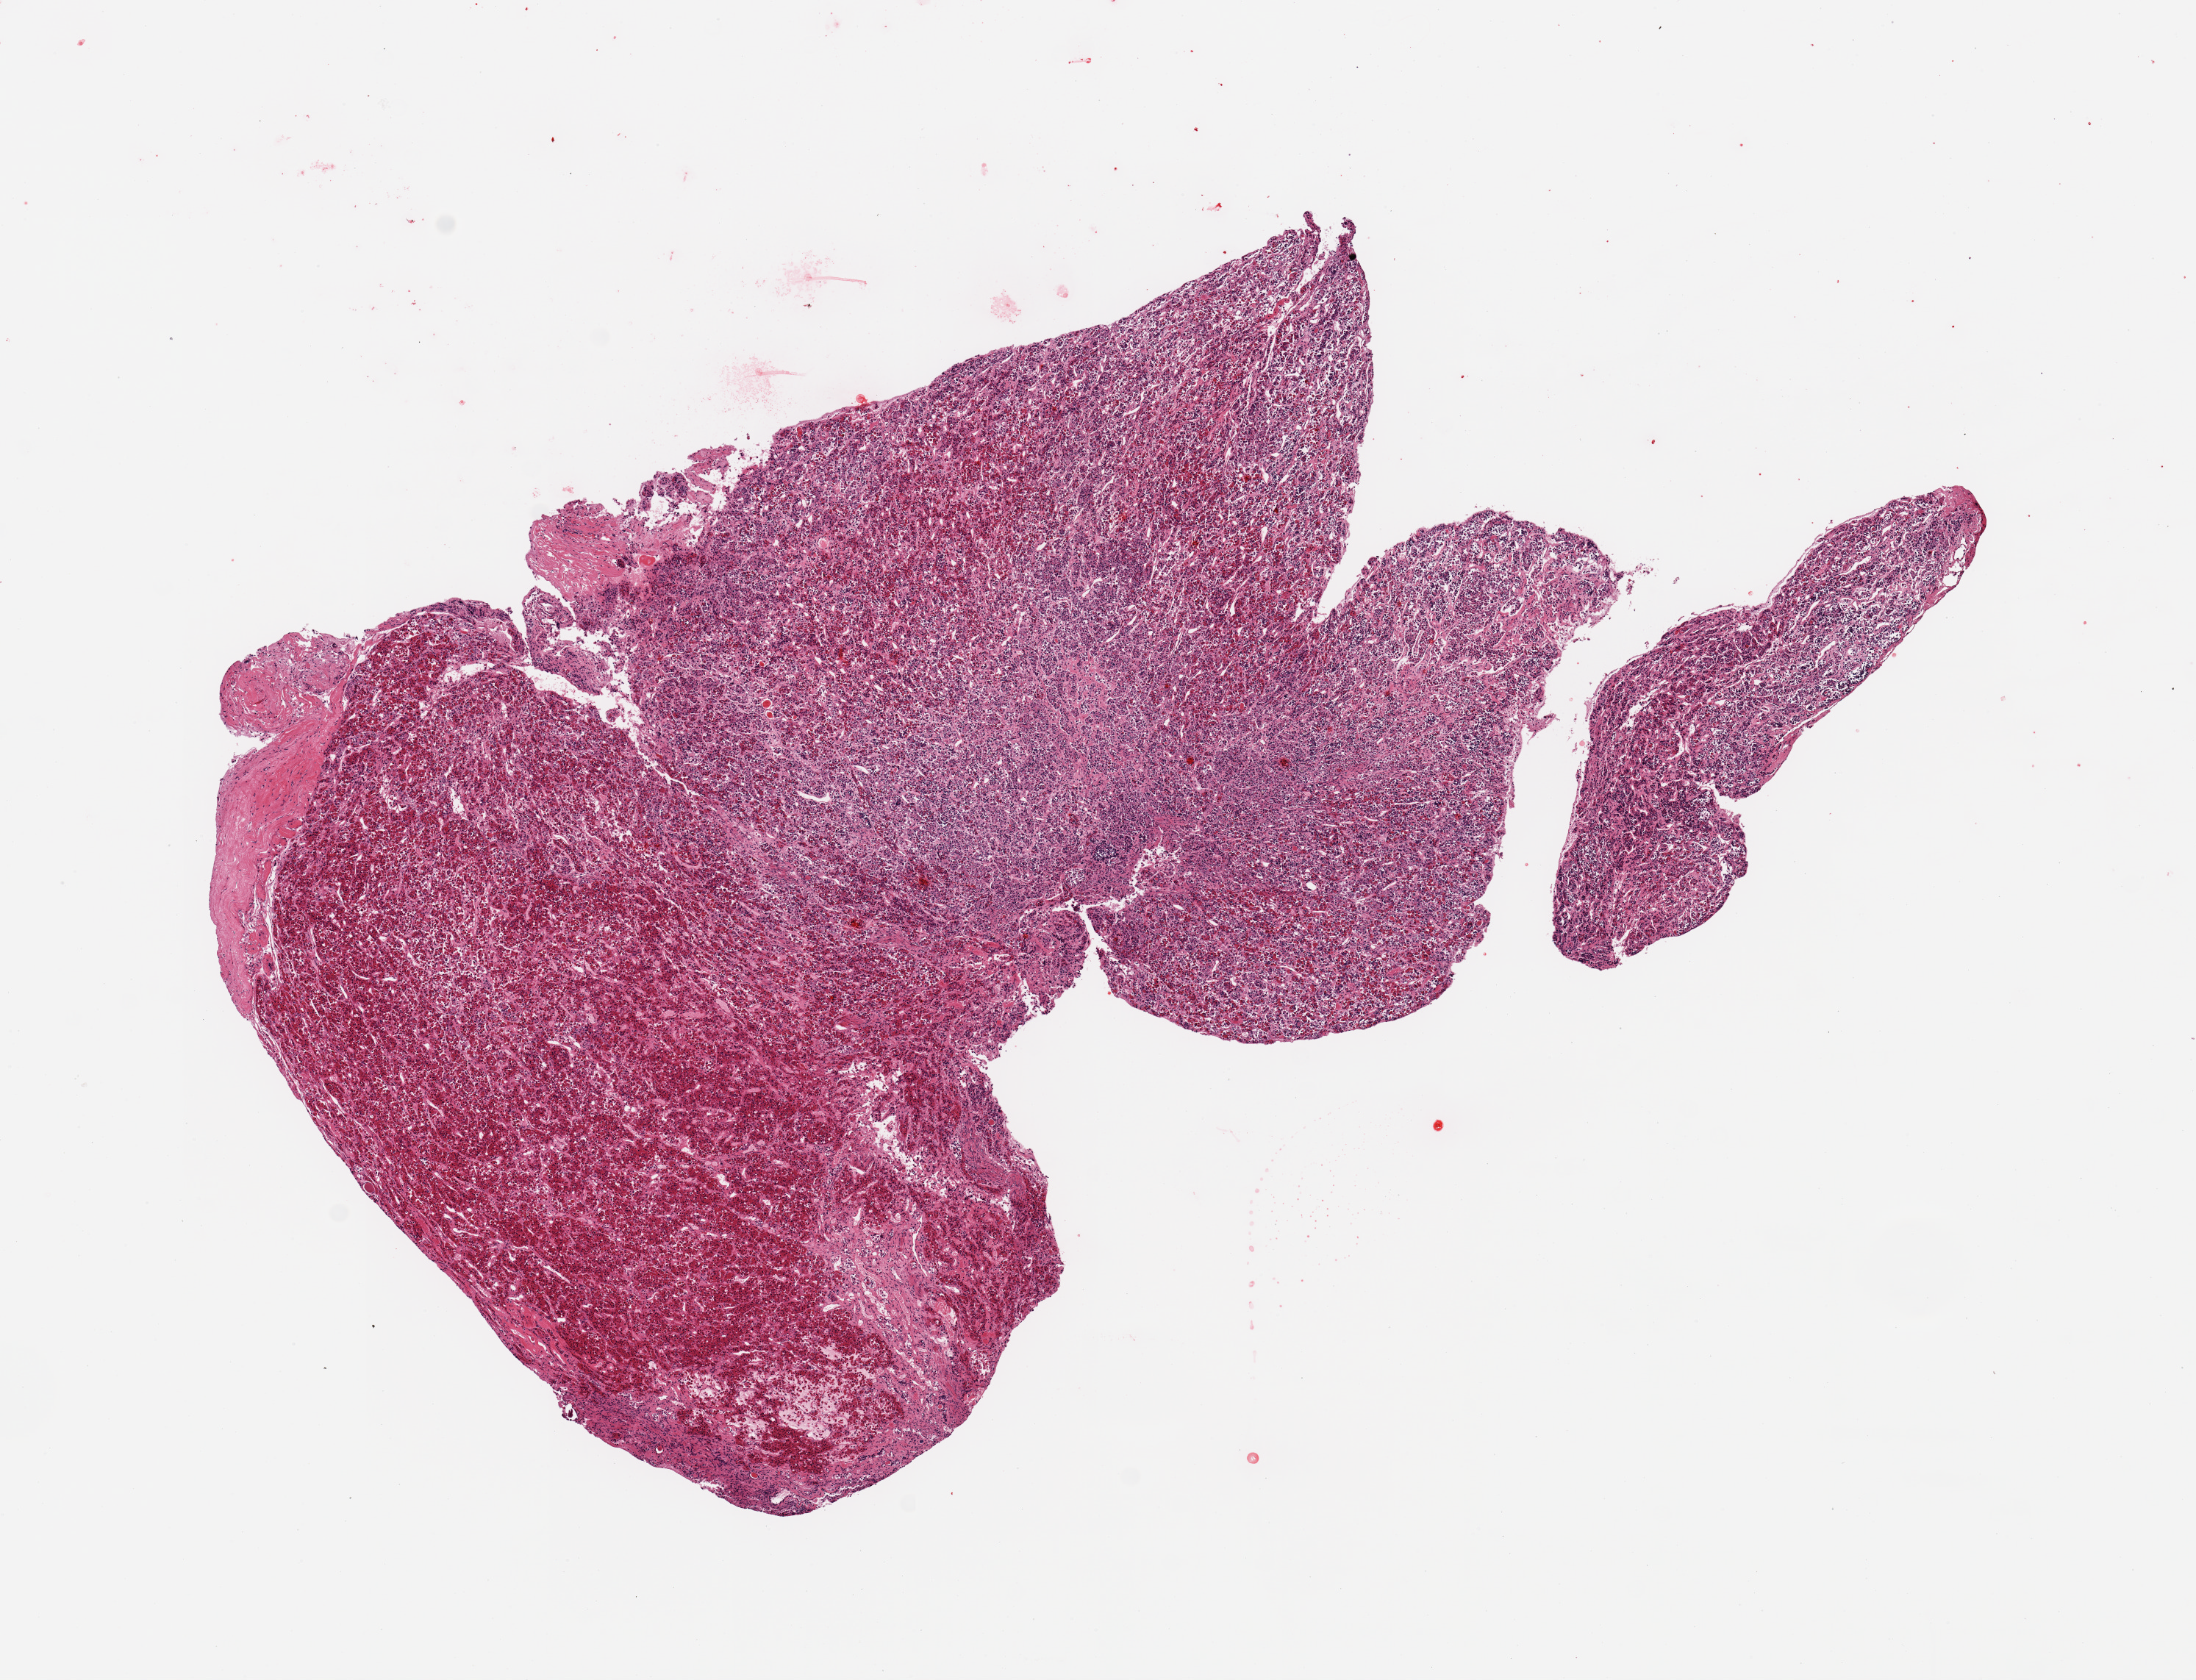
Whole-slide image, haematoxylin and eosin stain — a low-resolution overview of the entire scanned area, about 11.8 x 9.0 mm (from a 20x scan), PAXgene-fixed paraffin-embedded (PFPE) section, target tissue: pituitary, donor tissue sample. Female donor.
• review note (as recorded): 1 pieces, all adenohypophysis, moderately advanced autolysis